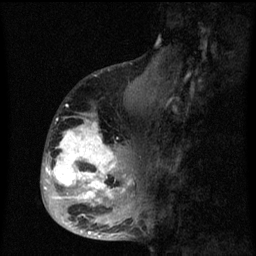
Breast MRI (dynamic contrast-enhanced), one sagittal slice; position 26 of 60 along the scan axis; dynamic contrast-enhanced series, image 2 of 3 at this slice position (ordered by acquisition); 1.5 T; TE 4.2 ms, TR 8 ms; 2 mm slice thickness; 256 × 256 image matrix, field of view 190 × 190 mm. Female patient, age 50 years.
Structures marked on this image (semi-automatically segmented with operator editing):
- analysis volume of interest (the breast-tissue region the enhancement analysis was run in; not a lesion): bounding box [x1, y1, x2, y2] px = [43, 90, 142, 216]
- tumour enhancement mask (voxels above the 70 % enhancement threshold inside the analysis volume of interest): [44, 121, 132, 216]